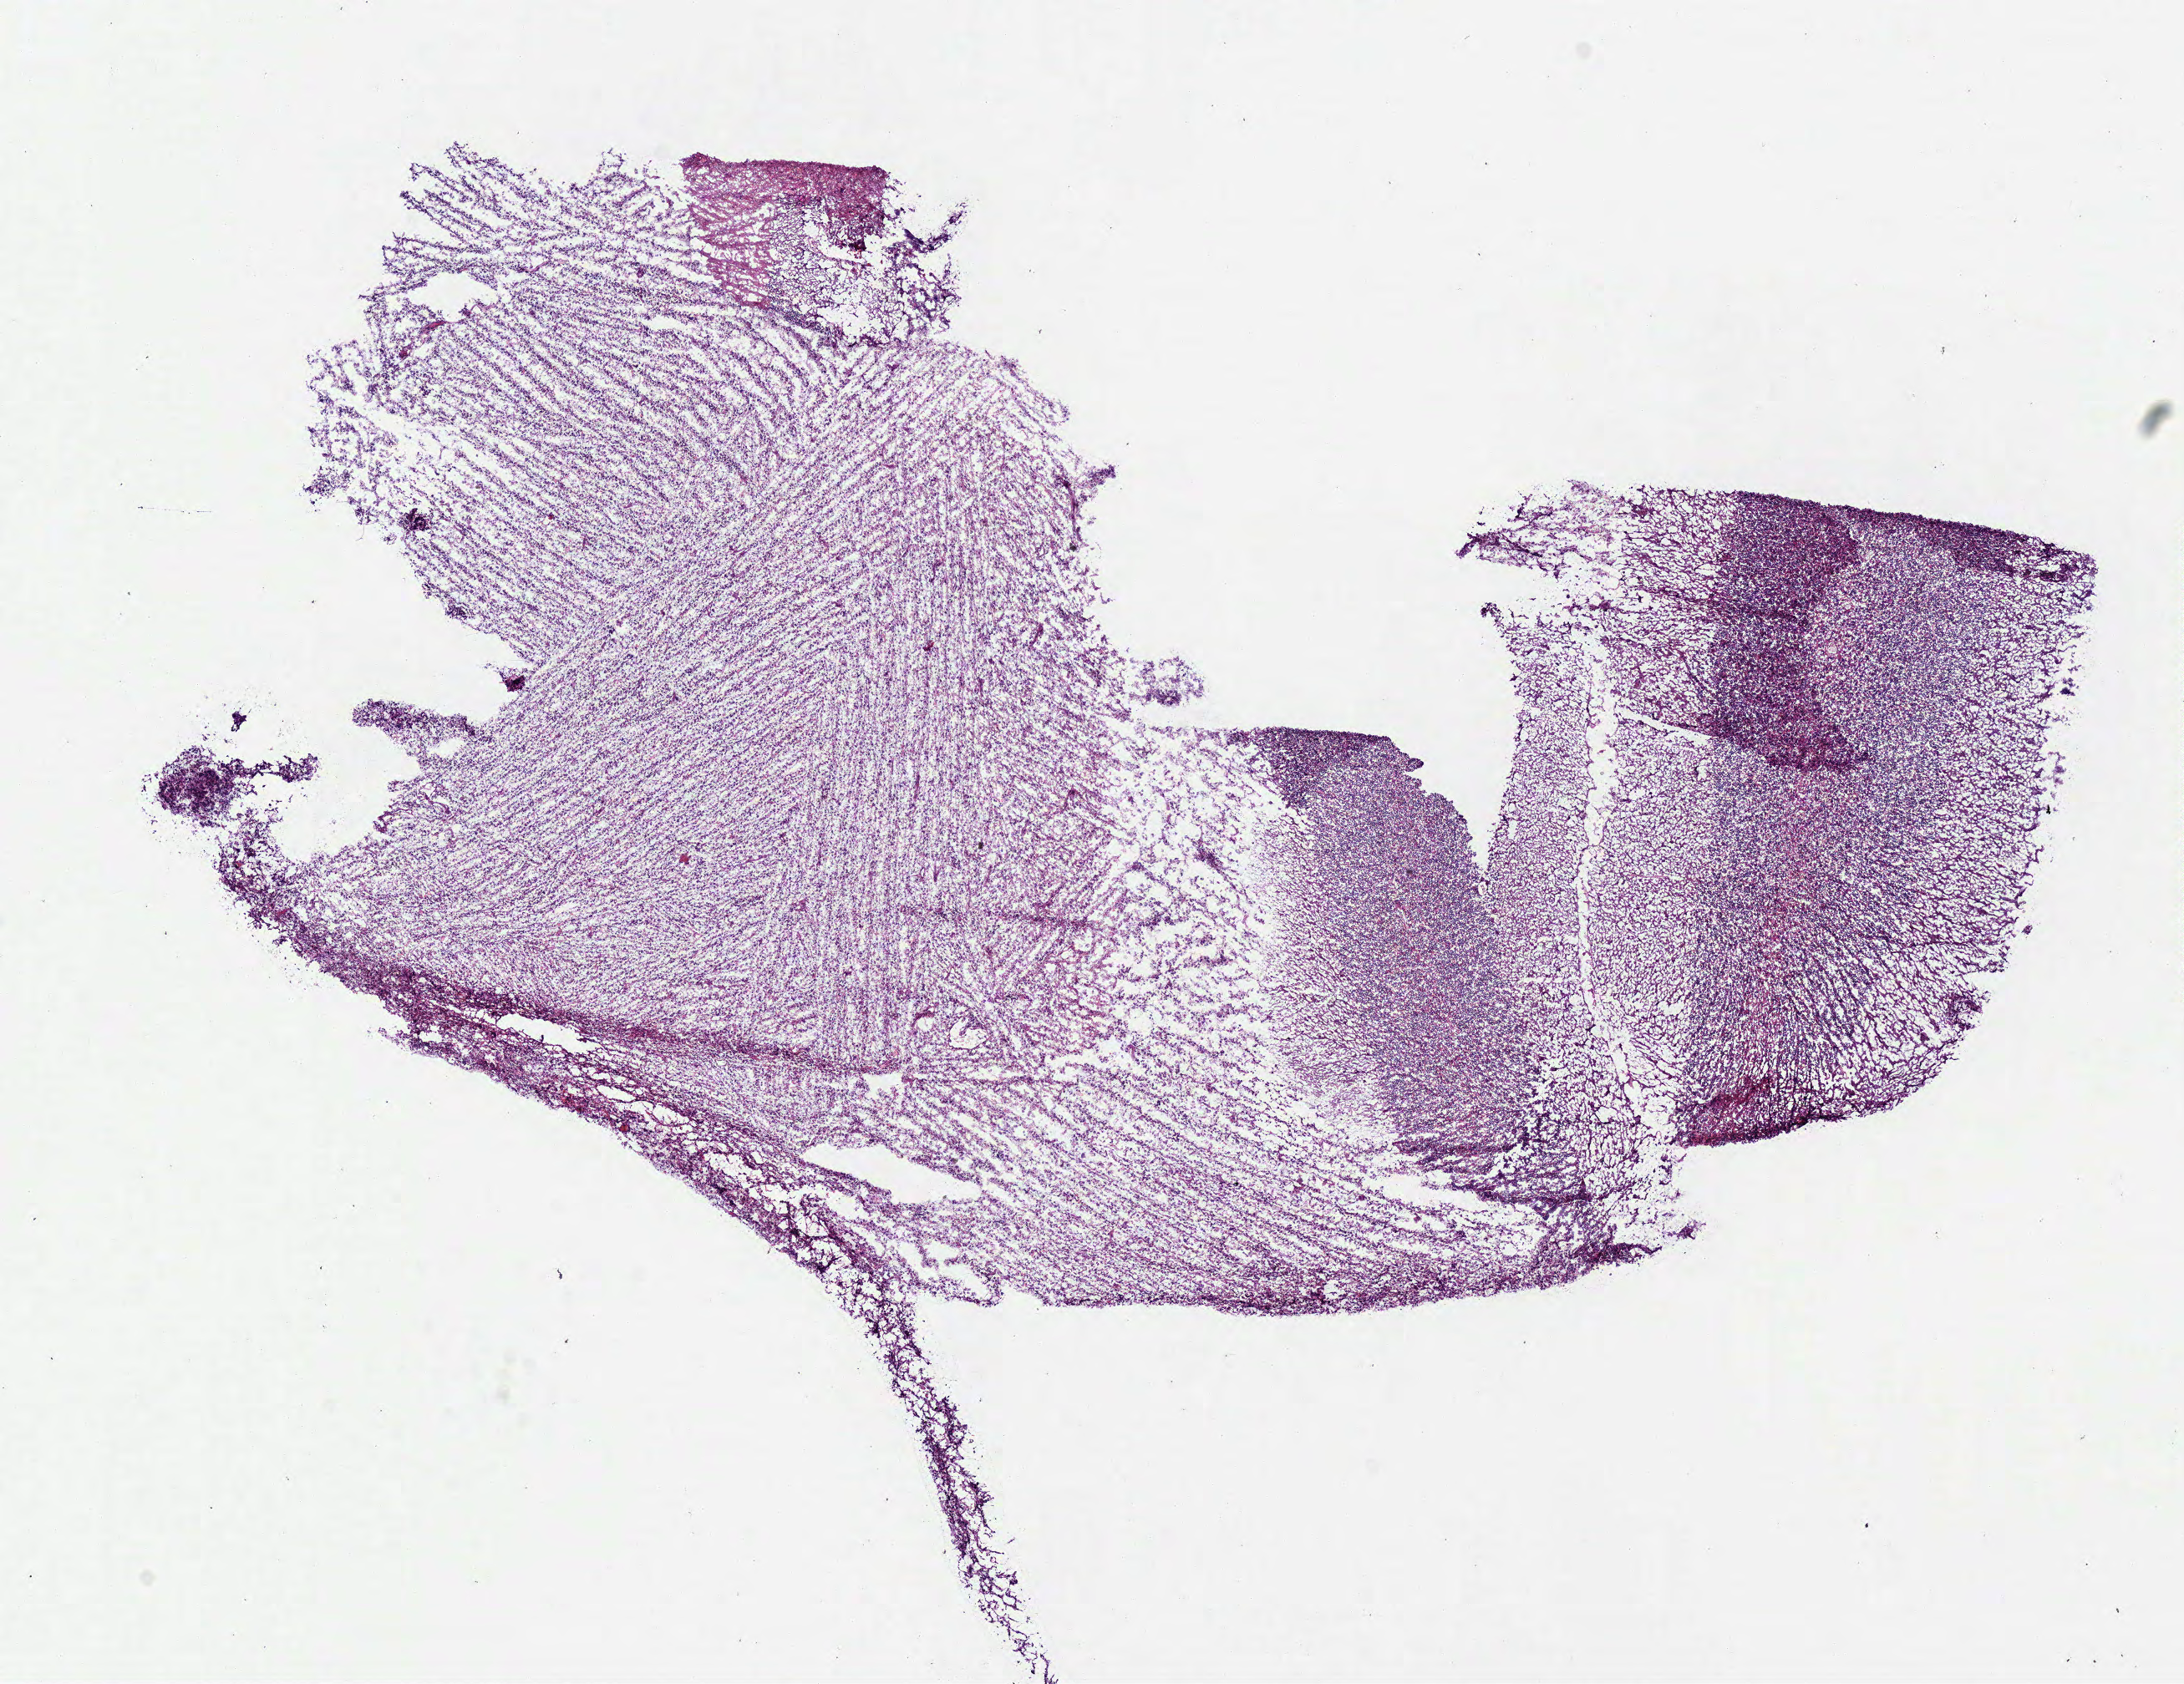
Whole-slide histology image, Hematoxylin and eosin (H&E) stained — whole scanned area (about 10.3 x 7.9 mm, from a 40x scan) shown as a low-resolution overview, frozen section from the bottom of the tissue portion, brain, primary tumour sample. Female patient; age at initial diagnosis 44 years. Pathologist review of this section (percent, as recorded): tumour cells 100%, tumour nuclei 85%, normal cells 0%, stromal cells 0%, necrosis 0%.
* histologic diagnosis: Glioblastoma